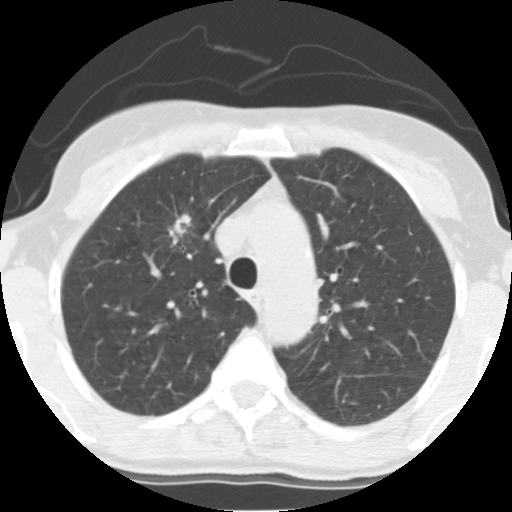
Axial slice from a low-dose chest CT screening exam; third annual screen; lung window (W 1500 / L -600 HU); standard (soft-tissue) reconstruction kernel (STANDARD); slice 40 of 140 in the series; 512 × 512 image matrix, field of view 280 × 280 mm. Female, age 56 years at enrolment. Former smoker at enrolment.
- Lesion marked by an expert reader, box from (x=158, y=208) to (x=203, y=255) px.
- Reader record for this screening exam (exam-level; its link to the box is not recorded): non-calcified nodule or mass ≥4 mm, right upper lobe, 17 × 12 mm, spiculated (stellate) margins, soft tissue attenuation, pre-existing on the prior screen: yes; interval growth: yes.
- Lung cancer was diagnosed 49 days after this screen: adenocarcinoma, NOS, right upper lobe, moderately differentiated (G2), stage IA (AJCC 6th edition), 19 mm at pathology.